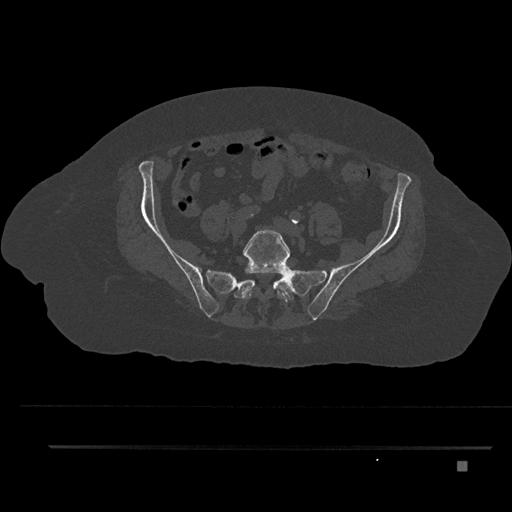
CT including the spine, one axial slice; slice 21 of 797 in the series (ordered by position); reconstruction kernel Br40s/3; bone window (W 1800 / L 400 HU); 512 × 512 image matrix, field of view 437 × 437 mm. Patient: female, 76 years. Case-level facts recorded for this patient, not image findings: primary cancer: lung.
Outlined on this slice (semi-automatically segmented with operator editing):
- L5 vertebra: bounding box <241,227,290,302> (left, top, right, bottom; pixels)